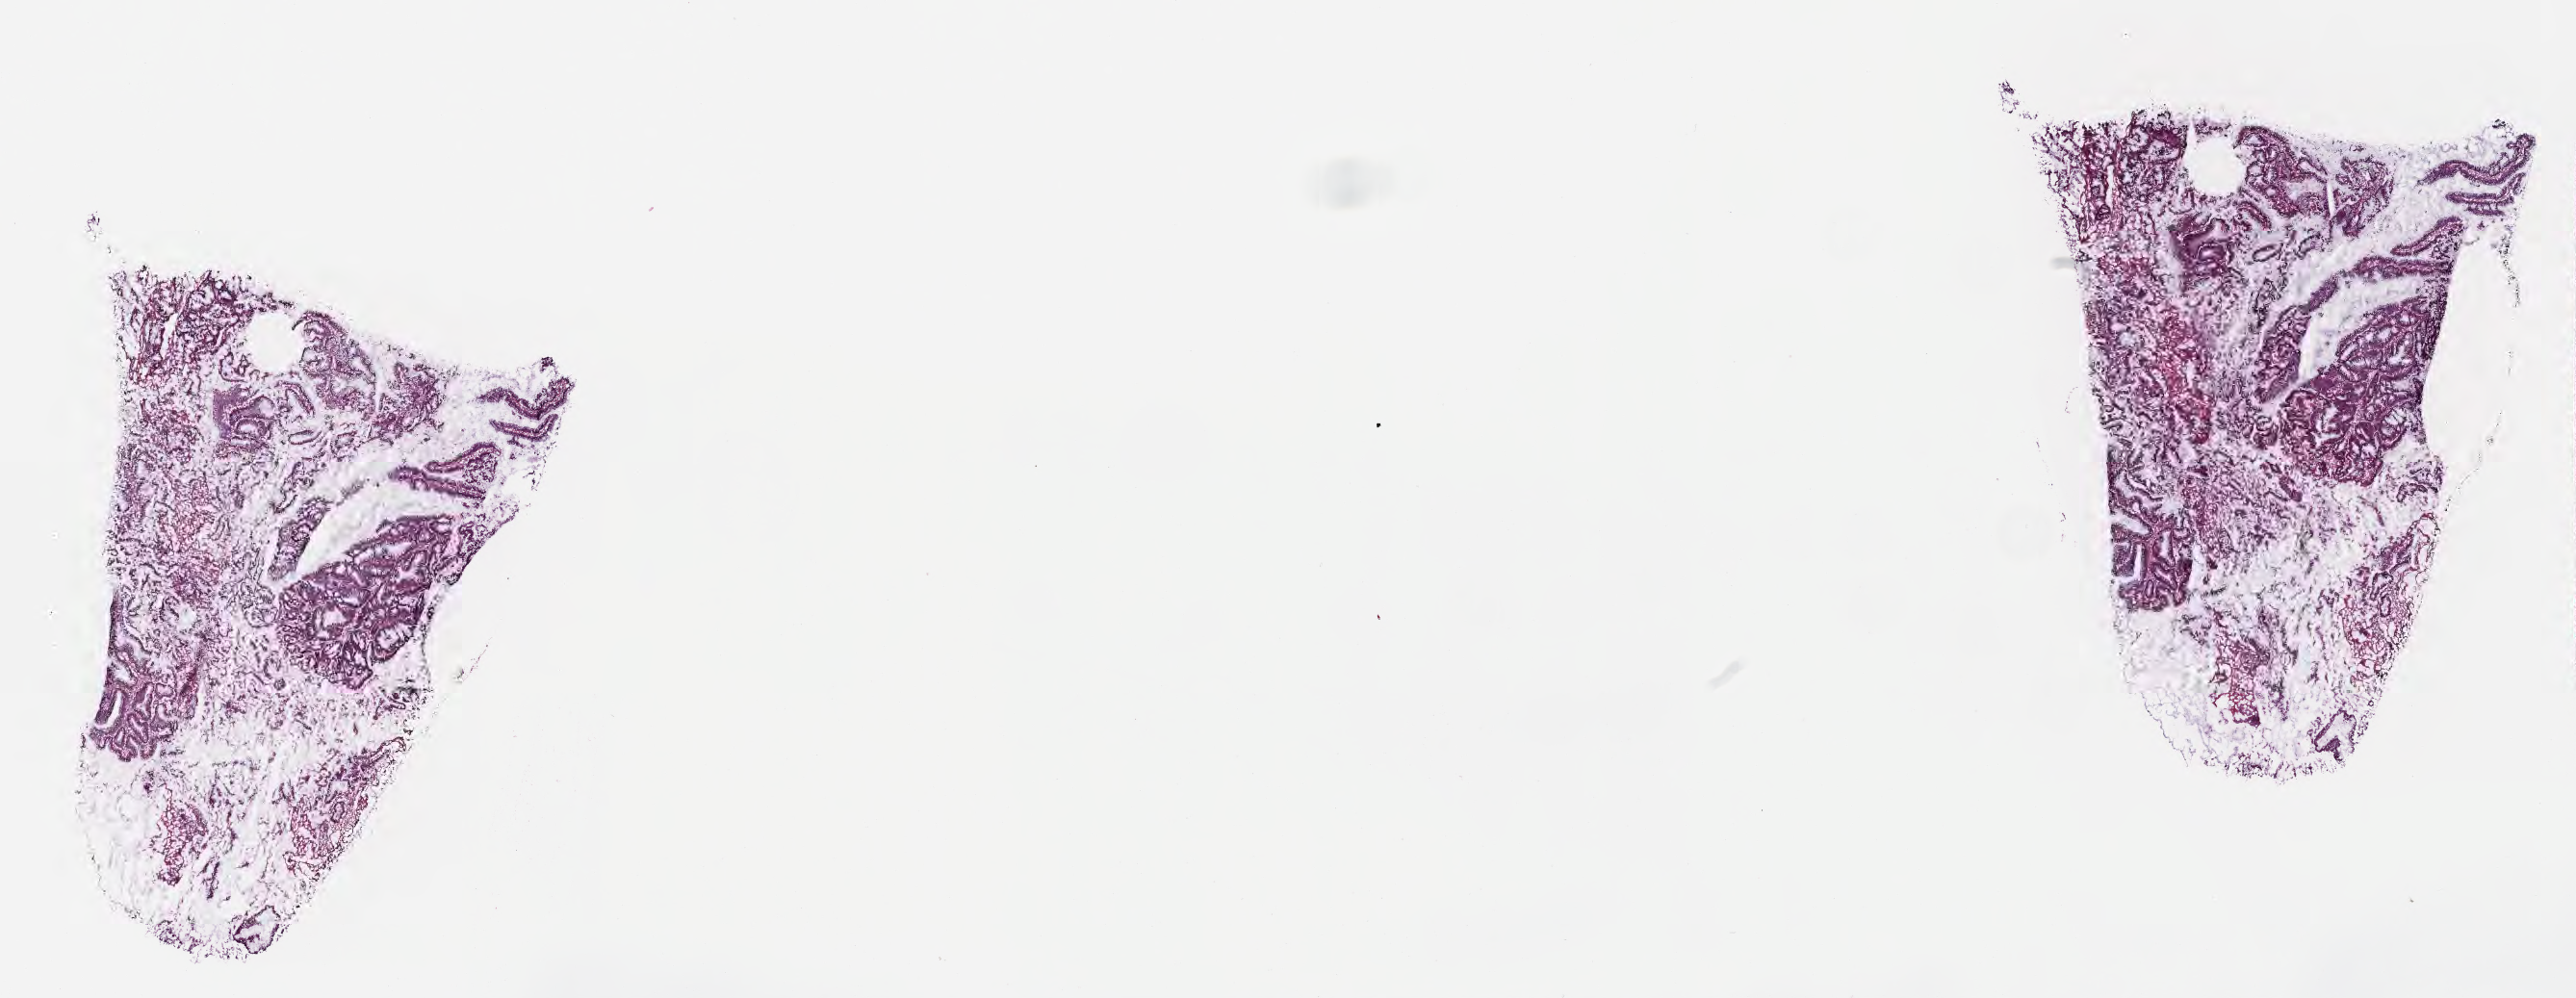
Digitized hematoxylin and eosin (H&E)-stained section, shown as a low-resolution overview of the whole scanned area (about 21.6 x 8.4 mm). Frozen section (tissue freezing medium). Specimen: premalignant lesion from a patient with serrated adenoma, NOS. Anatomic site: transverse colon. Male, age 54 years at initial diagnosis. Composition of this section per pathologist review: tumor cells 85%, tumor nuclei 85%, stromal cells 15%, necrosis 0%, normal cells 0%. Infiltration values recorded for this section: lymphocyte infiltration 3%, monocyte infiltration 2%, neutrophil infiltration 5%.
This section: sample classed premalignant; the patient's recorded diagnosis is given above. Section: bottom of the tissue portion.